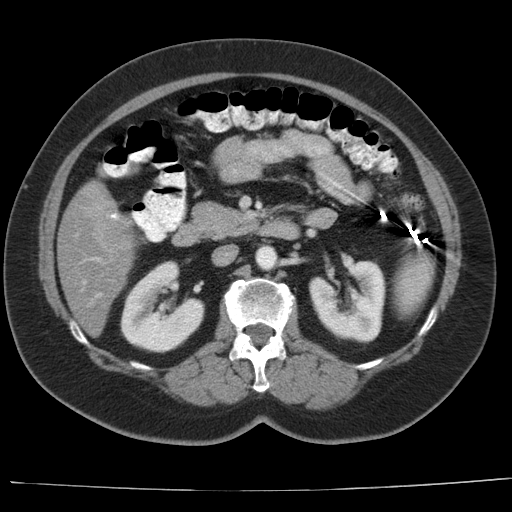
Contrast-enhanced abdominal CT, one axial slice; reconstruction kernel AA-1; intravenous contrast given; soft-tissue window (W 400 / L 40 HU); 5 mm slice thickness; 512 × 512 image matrix, field of view 373 × 373 mm. Female patient. From the clinical record (not read from this slice): diagnosis: colorectal cancer liver metastases, imaged before liver resection; multiple liver metastases: yes; largest metastasis: 1.8 cm.
Outlined on this slice (outlined manually by an expert reader):
- hepatic veins: bounding box [x1, y1, x2, y2] px = [82, 281, 86, 290]
- liver: [59, 181, 135, 335]
- portal vein (with intrahepatic branches): [96, 260, 113, 297]
- liver metastasis: [75, 192, 98, 209]
- liver metastasis: [102, 213, 130, 245]